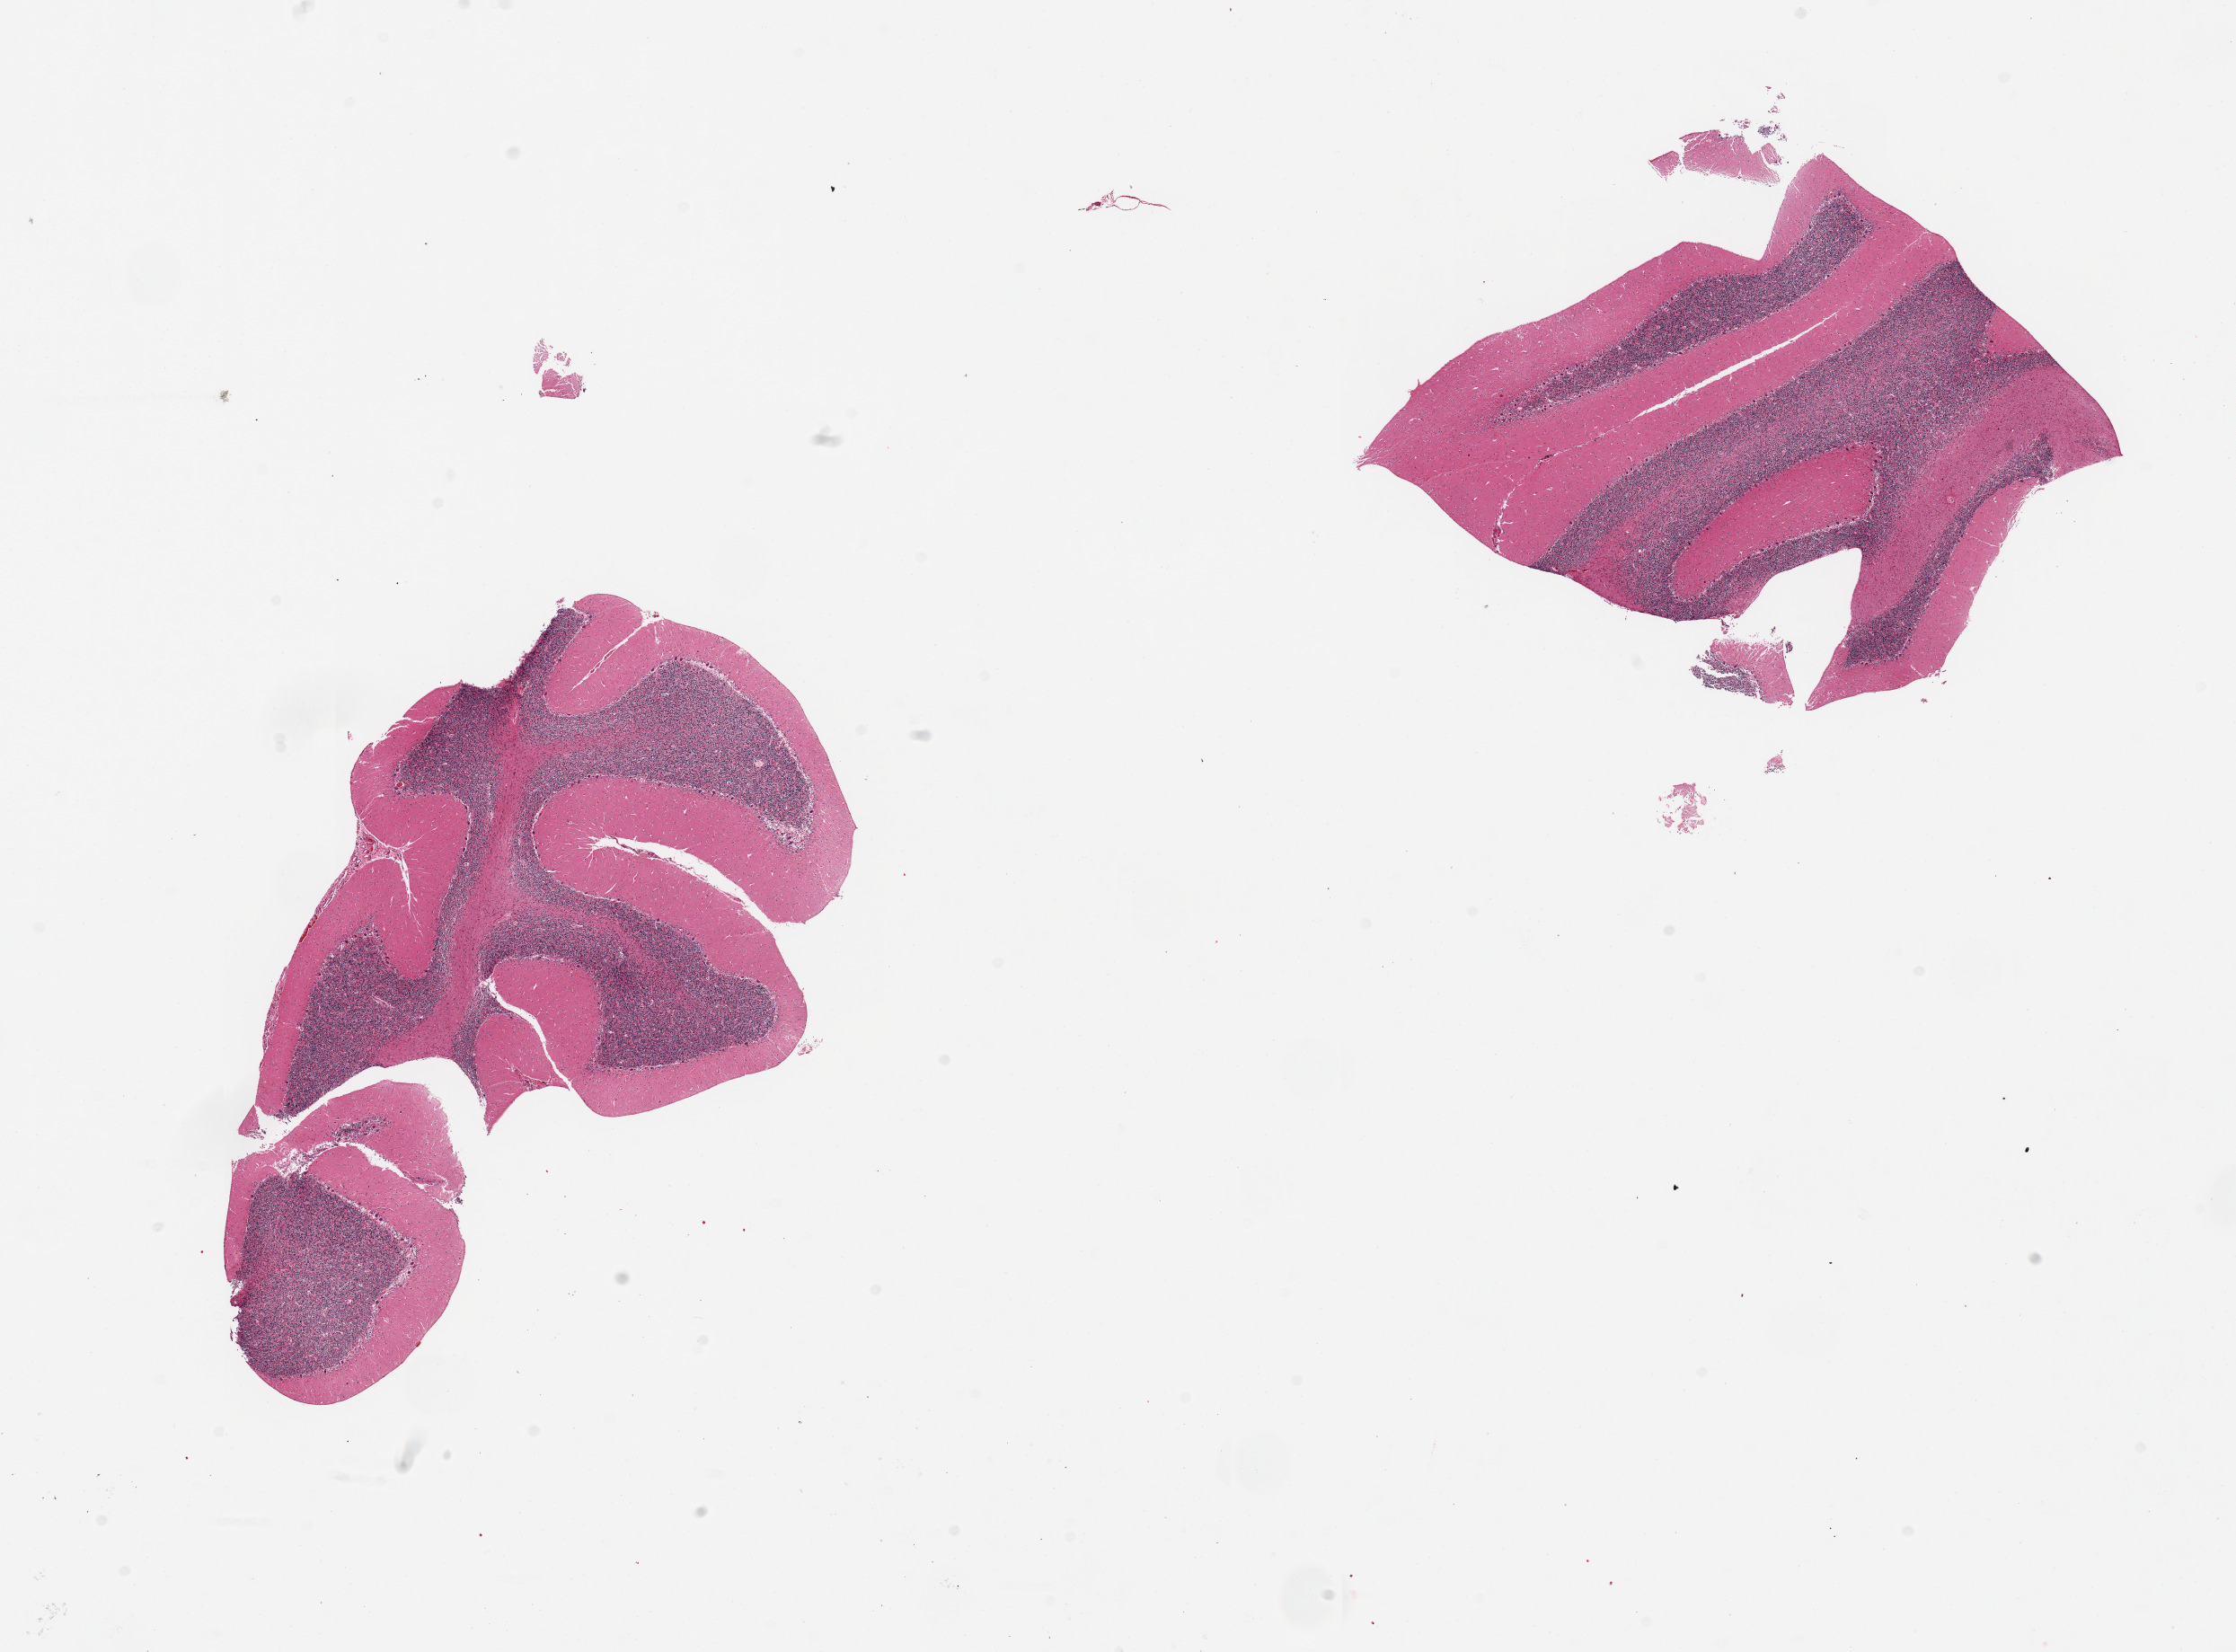
Haematoxylin and eosin whole-slide image, low-resolution overview of the scanned area, about 19.7 x 14.5 mm, PAXgene-fixed paraffin-embedded (PFPE) section, section of cerebellum (target tissue), tissue donor sample.
Pathologist's review note for this sample: 2 pieces.